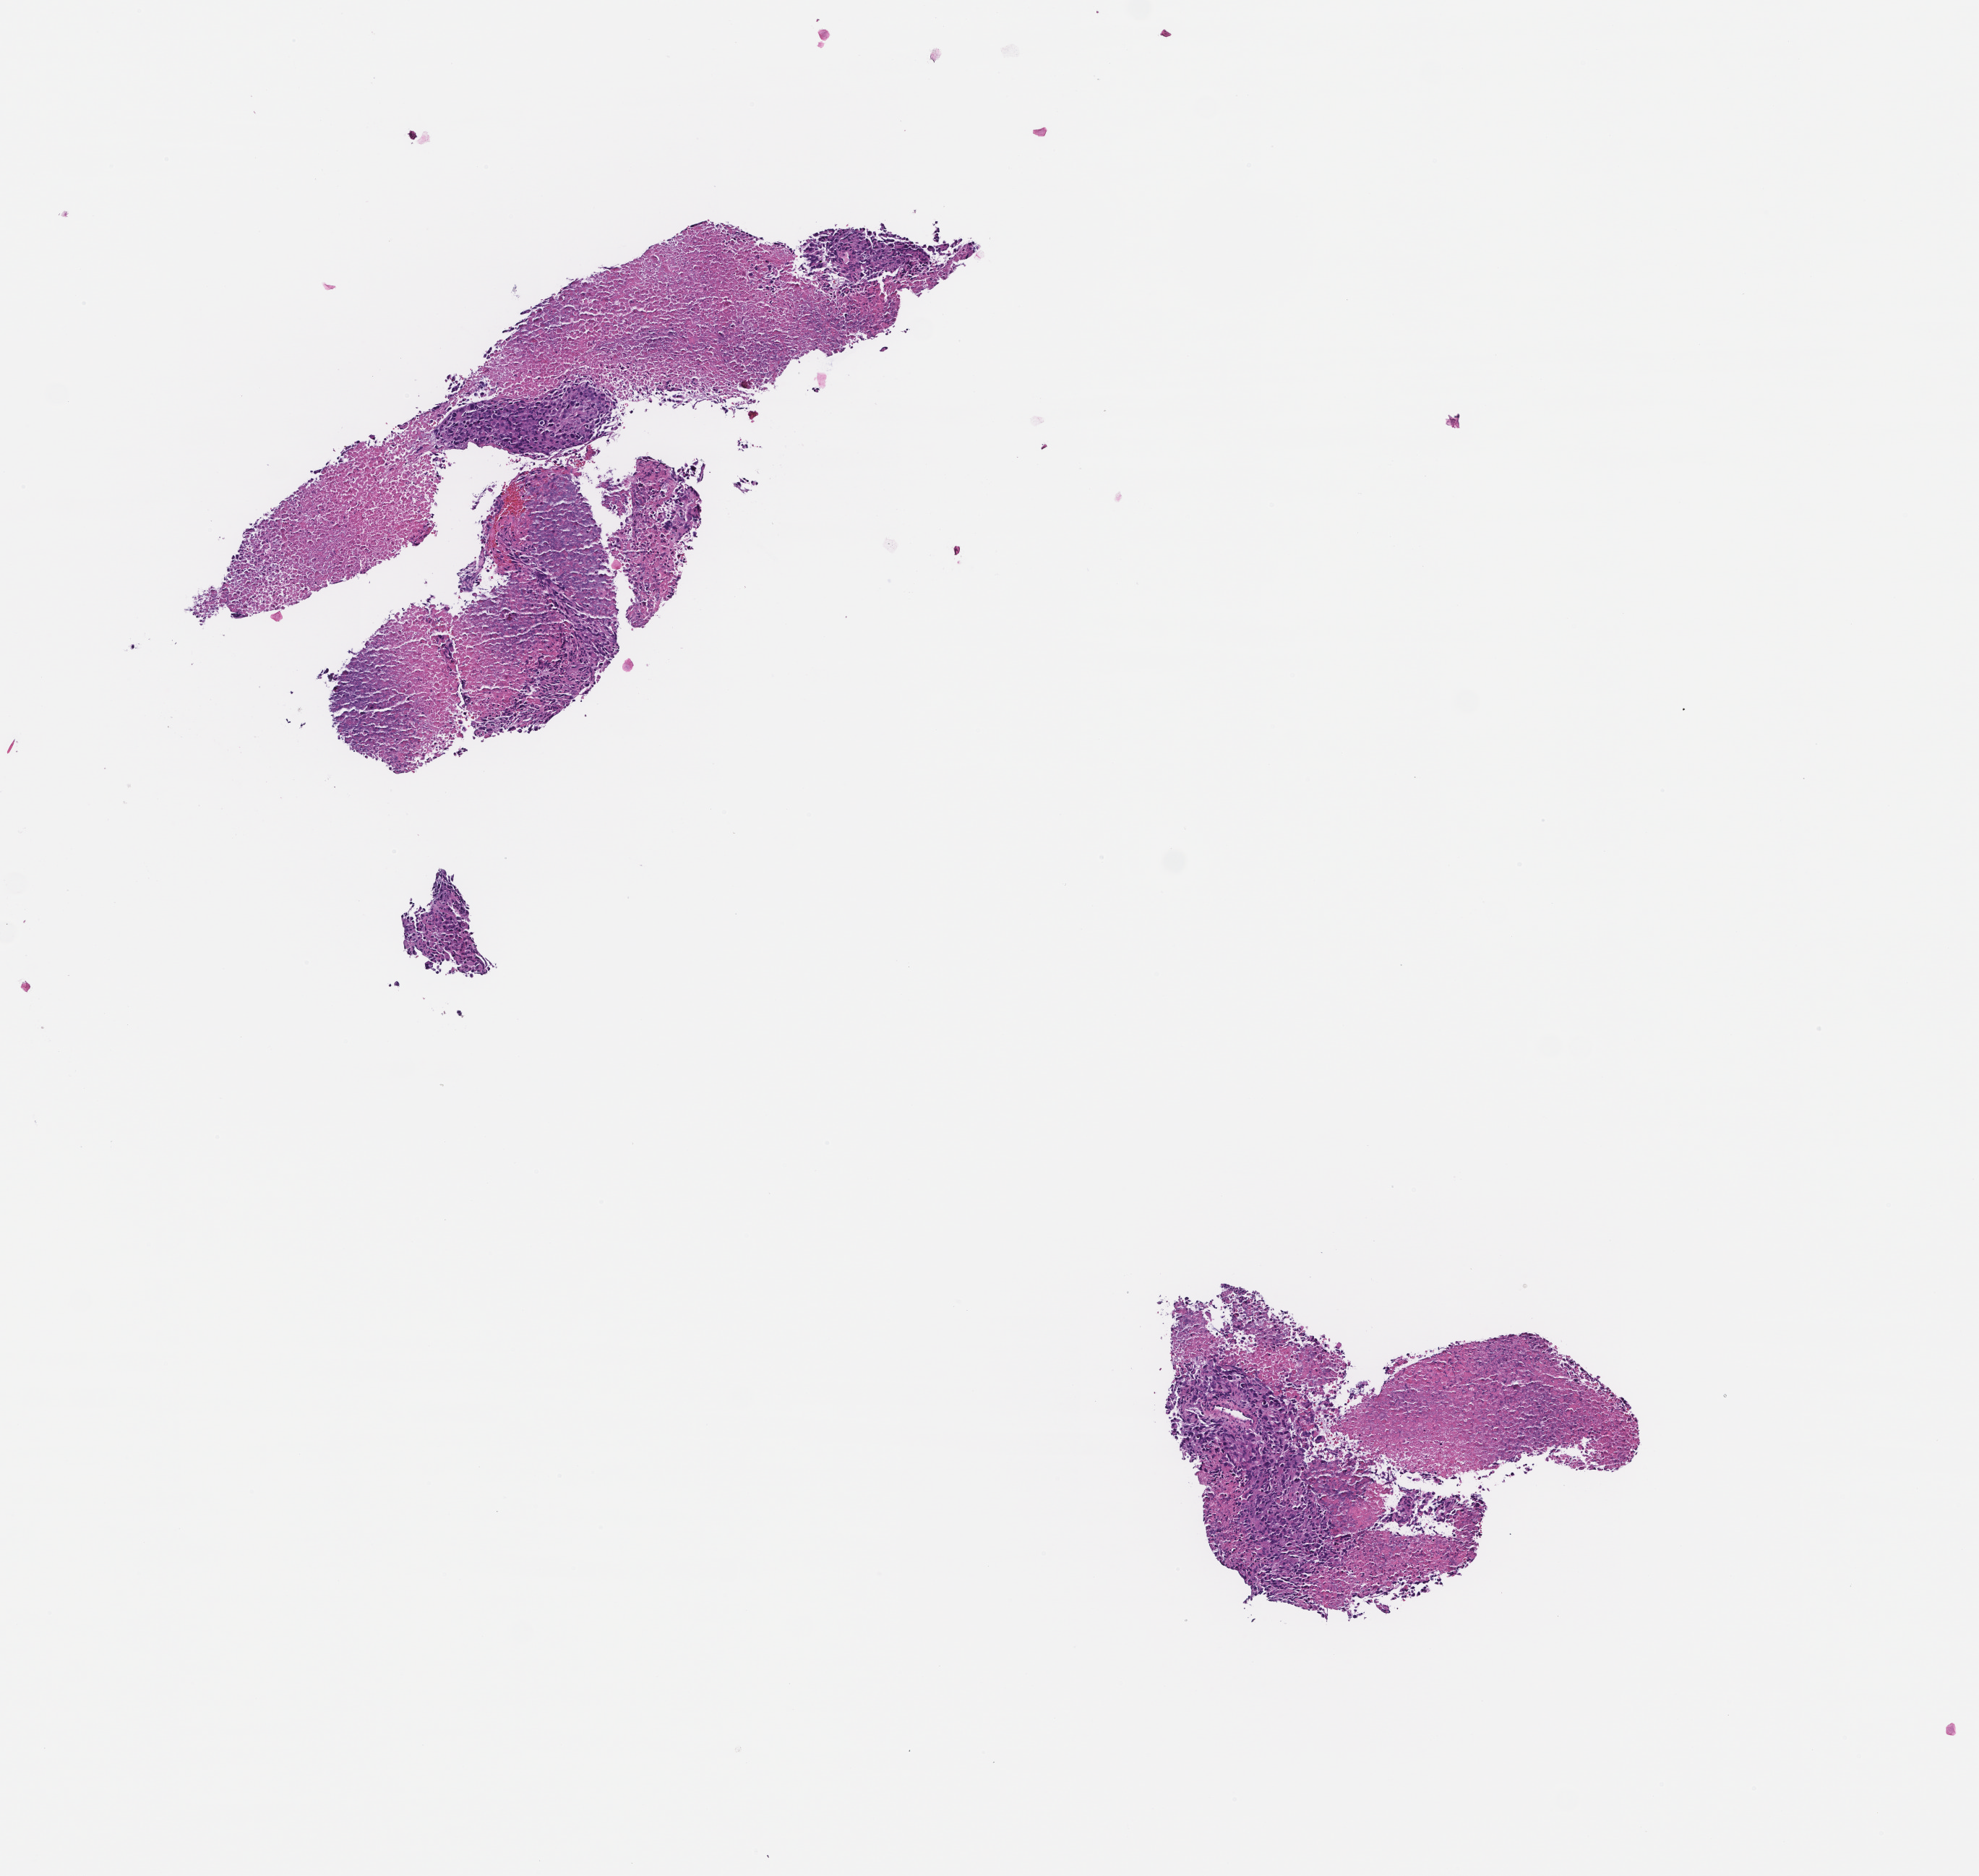
H&E whole-slide image, low-resolution overview of the scanned area, about 5.5 x 5.2 mm, formalin-fixed, paraffin-embedded (FFPE) tissue, collected at disease progression. Male patient.
This section: metastatic tumor tissue. Primary diagnosis of the patient: Non-Small Cell Lung Carcinoma.